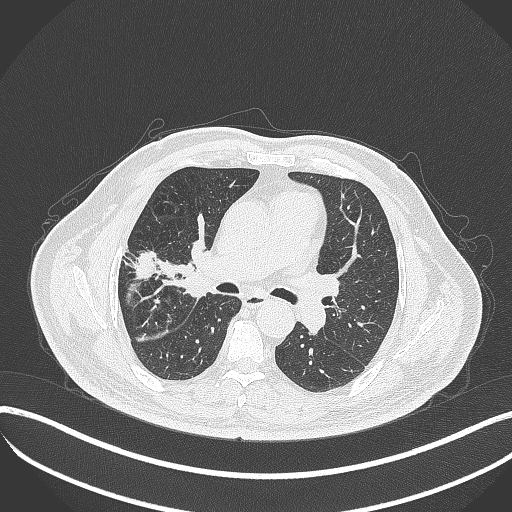
Chest CT, one axial slice; slice 211 of 401 in the series (ordered by position); 120 kVp; lung window (W 1500 / L -600 HU); 1 mm slice thickness; 512 × 512 image matrix. Patient: male, 72 years. From the clinical record (not read from this slice): clinical TNM (as recorded): T1c N0 M0; histopathological grade: G2.
Outlined on this slice (rectangle marked by the reading radiologist):
- lung tumour (recorded histology: squamous cell carcinoma): bounding box <171,240,210,304> (left, top, right, bottom; pixels)